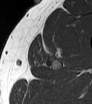
MRI of an extremity soft-tissue mass, one axial slice. Slice 47 of 62 in the series (ordered by position). MR volume resampled by the dataset authors to the PET/CT grid (not the native acquisition matrix). 3.27 mm slice thickness. 92 × 104 image matrix. Male patient. Case-level facts recorded for this patient, not image findings: histological type: mixoid liposarcoma; grade: low; site of the primary tumour: left thigh.
Outlined on this slice (expert contour drawn on MRI and transferred to this co-registered scan by the dataset authors):
- gross tumour volume (mass): box from (x=44, y=44) to (x=61, y=57) px